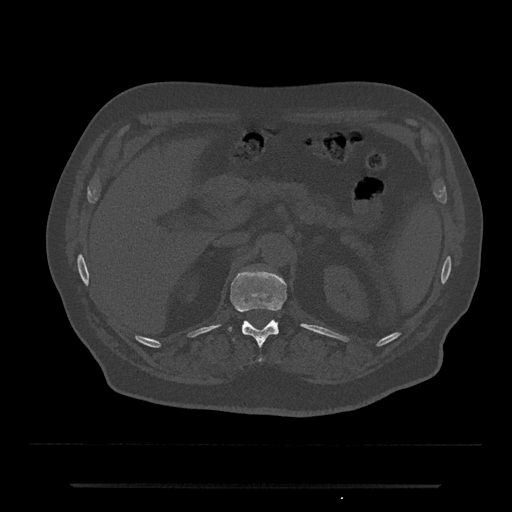
CT including the spine, one axial slice; position 586 of 797 along the scan axis; reconstruction kernel Br40s/3; 120 kVp; bone window (W 1800 / L 400 HU); 0.5 mm slice thickness; 512 × 512 image matrix, field of view 434 × 434 mm. Male patient, age 80 years. Case-level facts recorded for this patient, not image findings: primary cancer: prostate; vertebrae with lytic lesions (as recorded): L1, T11.
Annotated regions visible in this slice (semi-automatic segmentation, software-assisted and operator-edited):
- T12 vertebra: bounding box (x1, y1, x2, y2) in pixels: (229, 272, 287, 362)